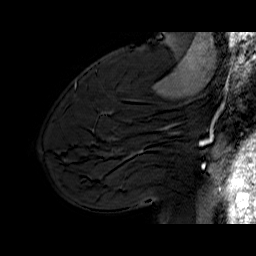
Breast MRI (dynamic contrast-enhanced), one sagittal slice; position 43 of 70 along the scan axis; dynamic contrast-enhanced series, time point 2 of 6 at this slice position (early post-contrast); 1.5 T; TE 6.5 ms, TR 33 ms; 4 mm slice thickness; 256 × 256 image matrix. Female patient. Case-level facts recorded for this patient, not image findings: setting: breast cancer imaged before/during neoadjuvant chemotherapy; receptor status: HER2-positive.
Outlined on this slice (semi-automatic segmentation, software-assisted and operator-edited):
- analysis volume of interest (the breast-tissue region the enhancement analysis was run in; not a lesion): bounding box [x1, y1, x2, y2] px = [113, 112, 174, 170]
- tumour enhancement mask (voxels above the 100 % enhancement threshold inside the analysis volume of interest): [163, 124, 174, 134]